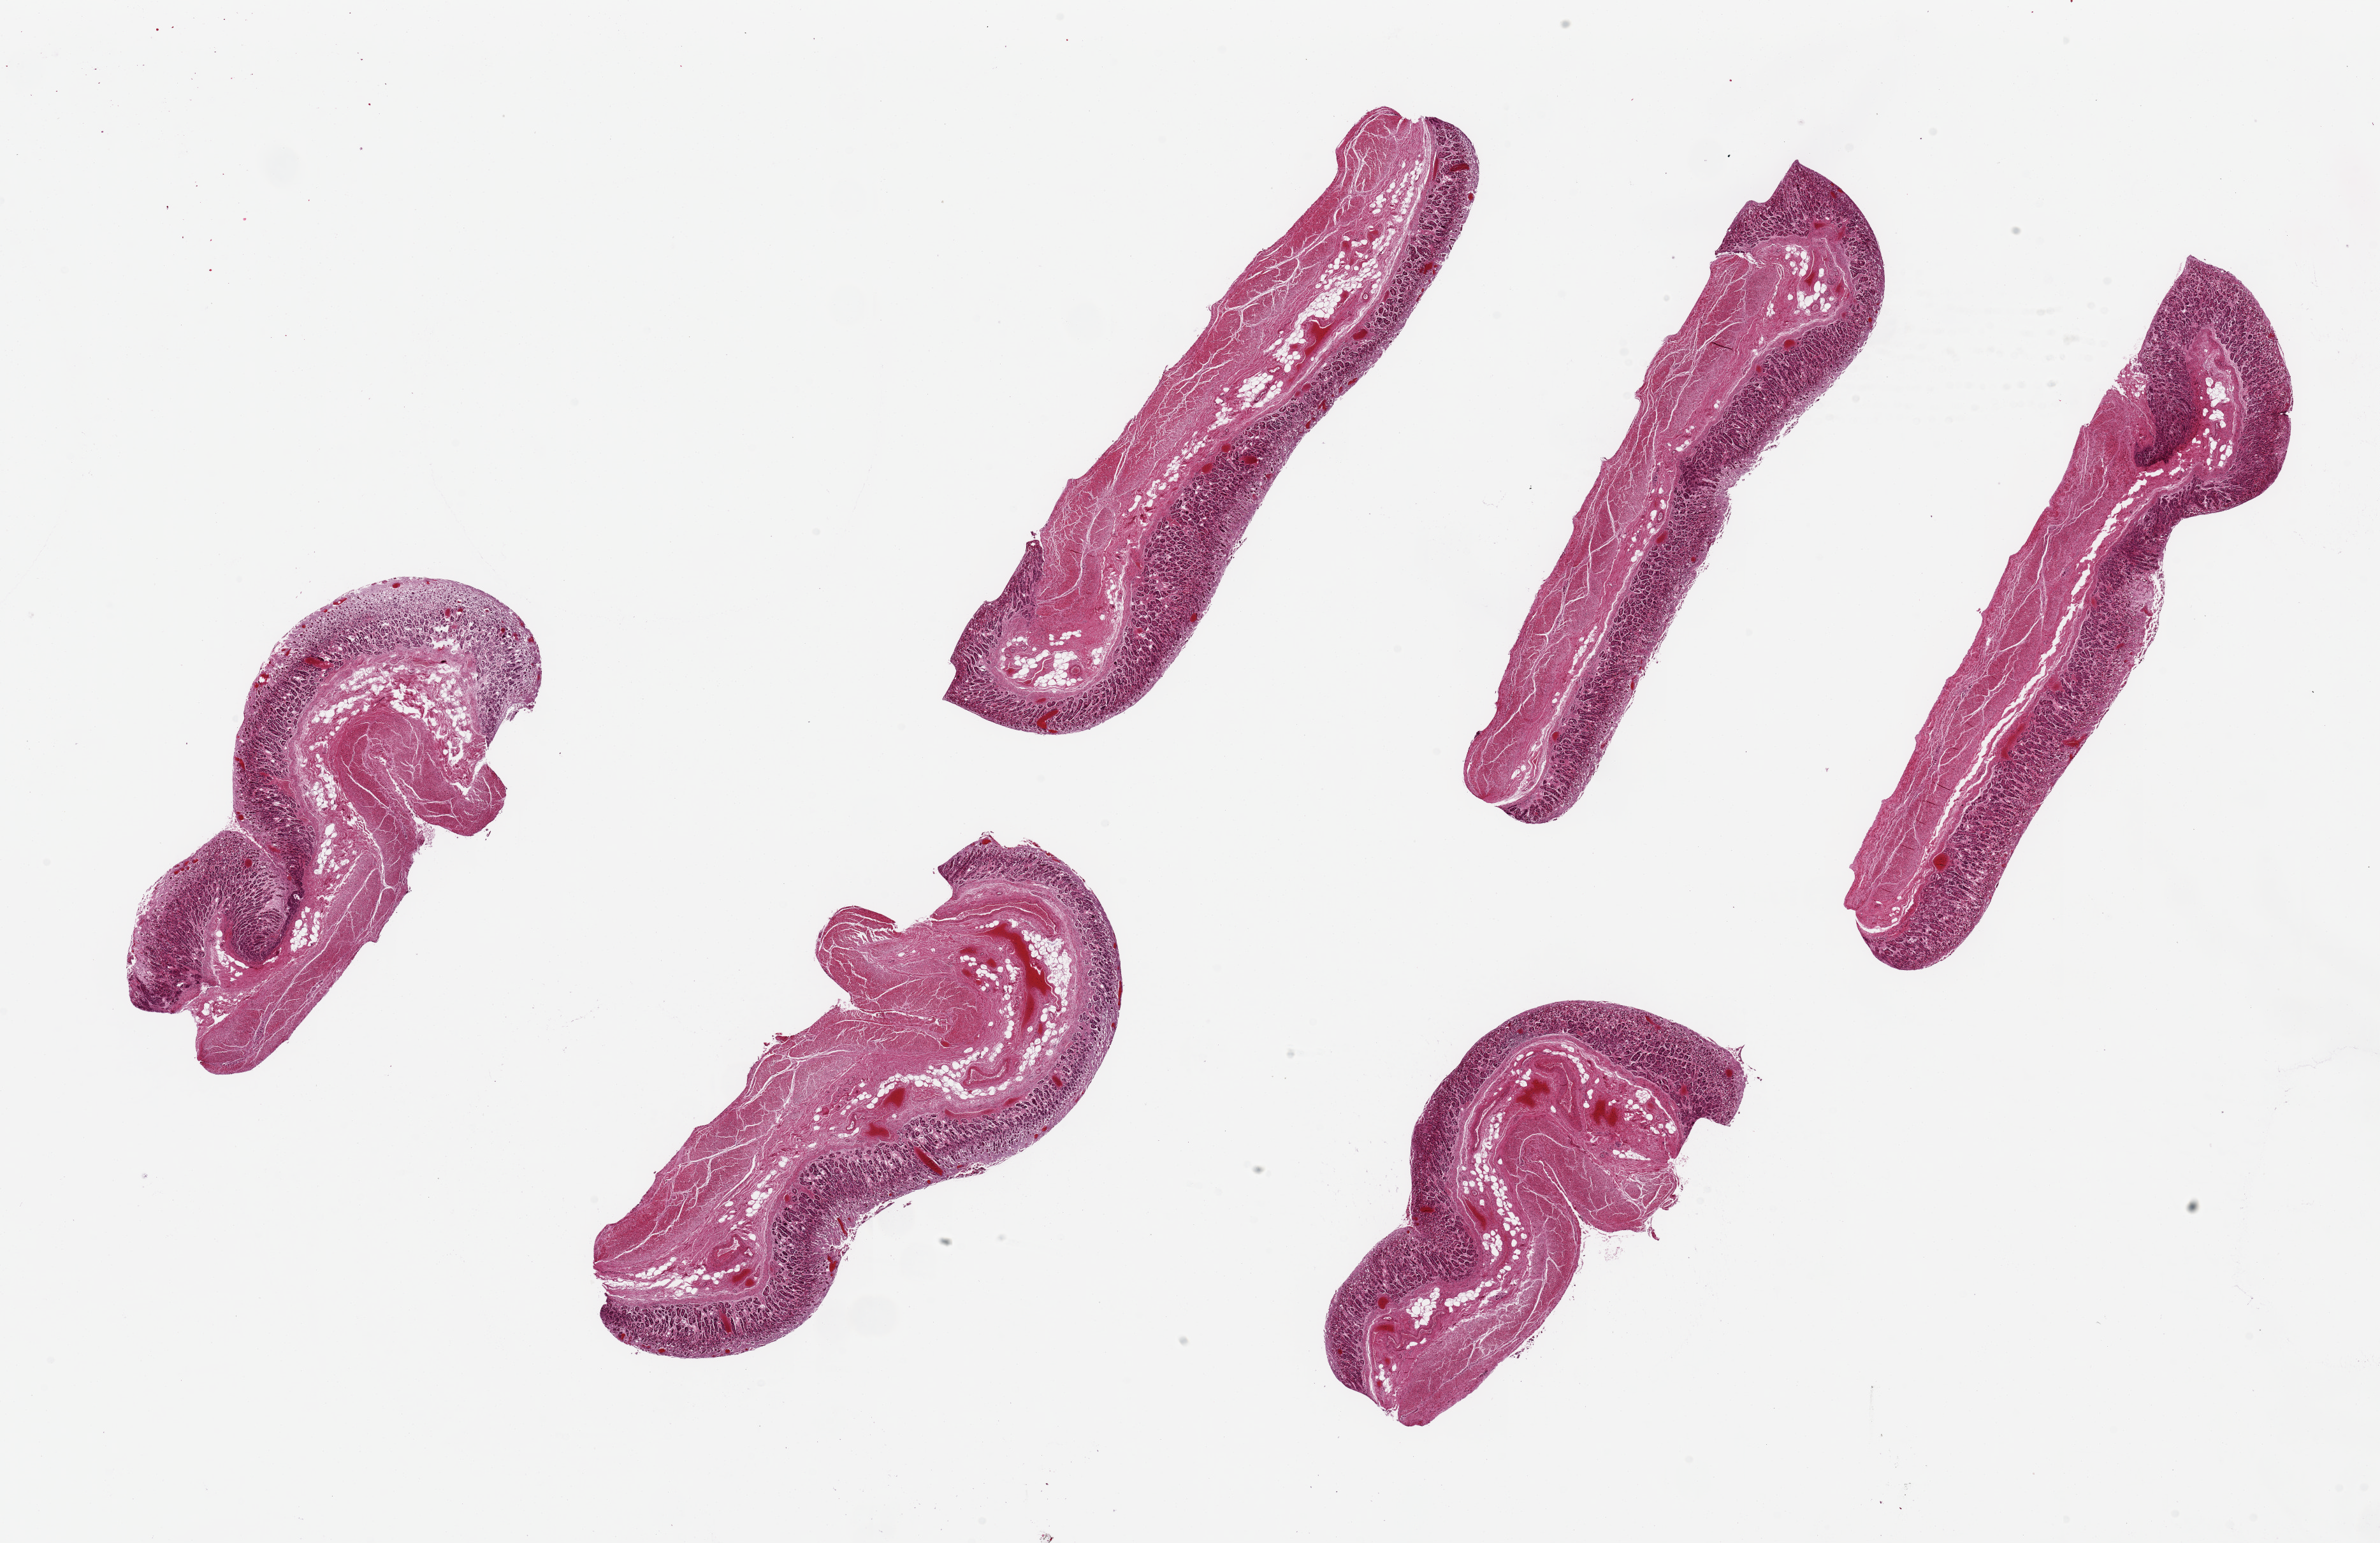
Digitized haematoxylin and eosin-stained section, brightfield, shown as a low-resolution overview of the whole scanned area (about 29.5 x 19.1 mm); PAXgene-fixed paraffin-embedded (PFPE) section; target tissue: stomach; donor tissue sample. Male donor.
- reviewer comment on this tissue sample: 6 pieces ~8x1.5mm, mucosa up to 50% thickness of some pieces but all badly autolyzed